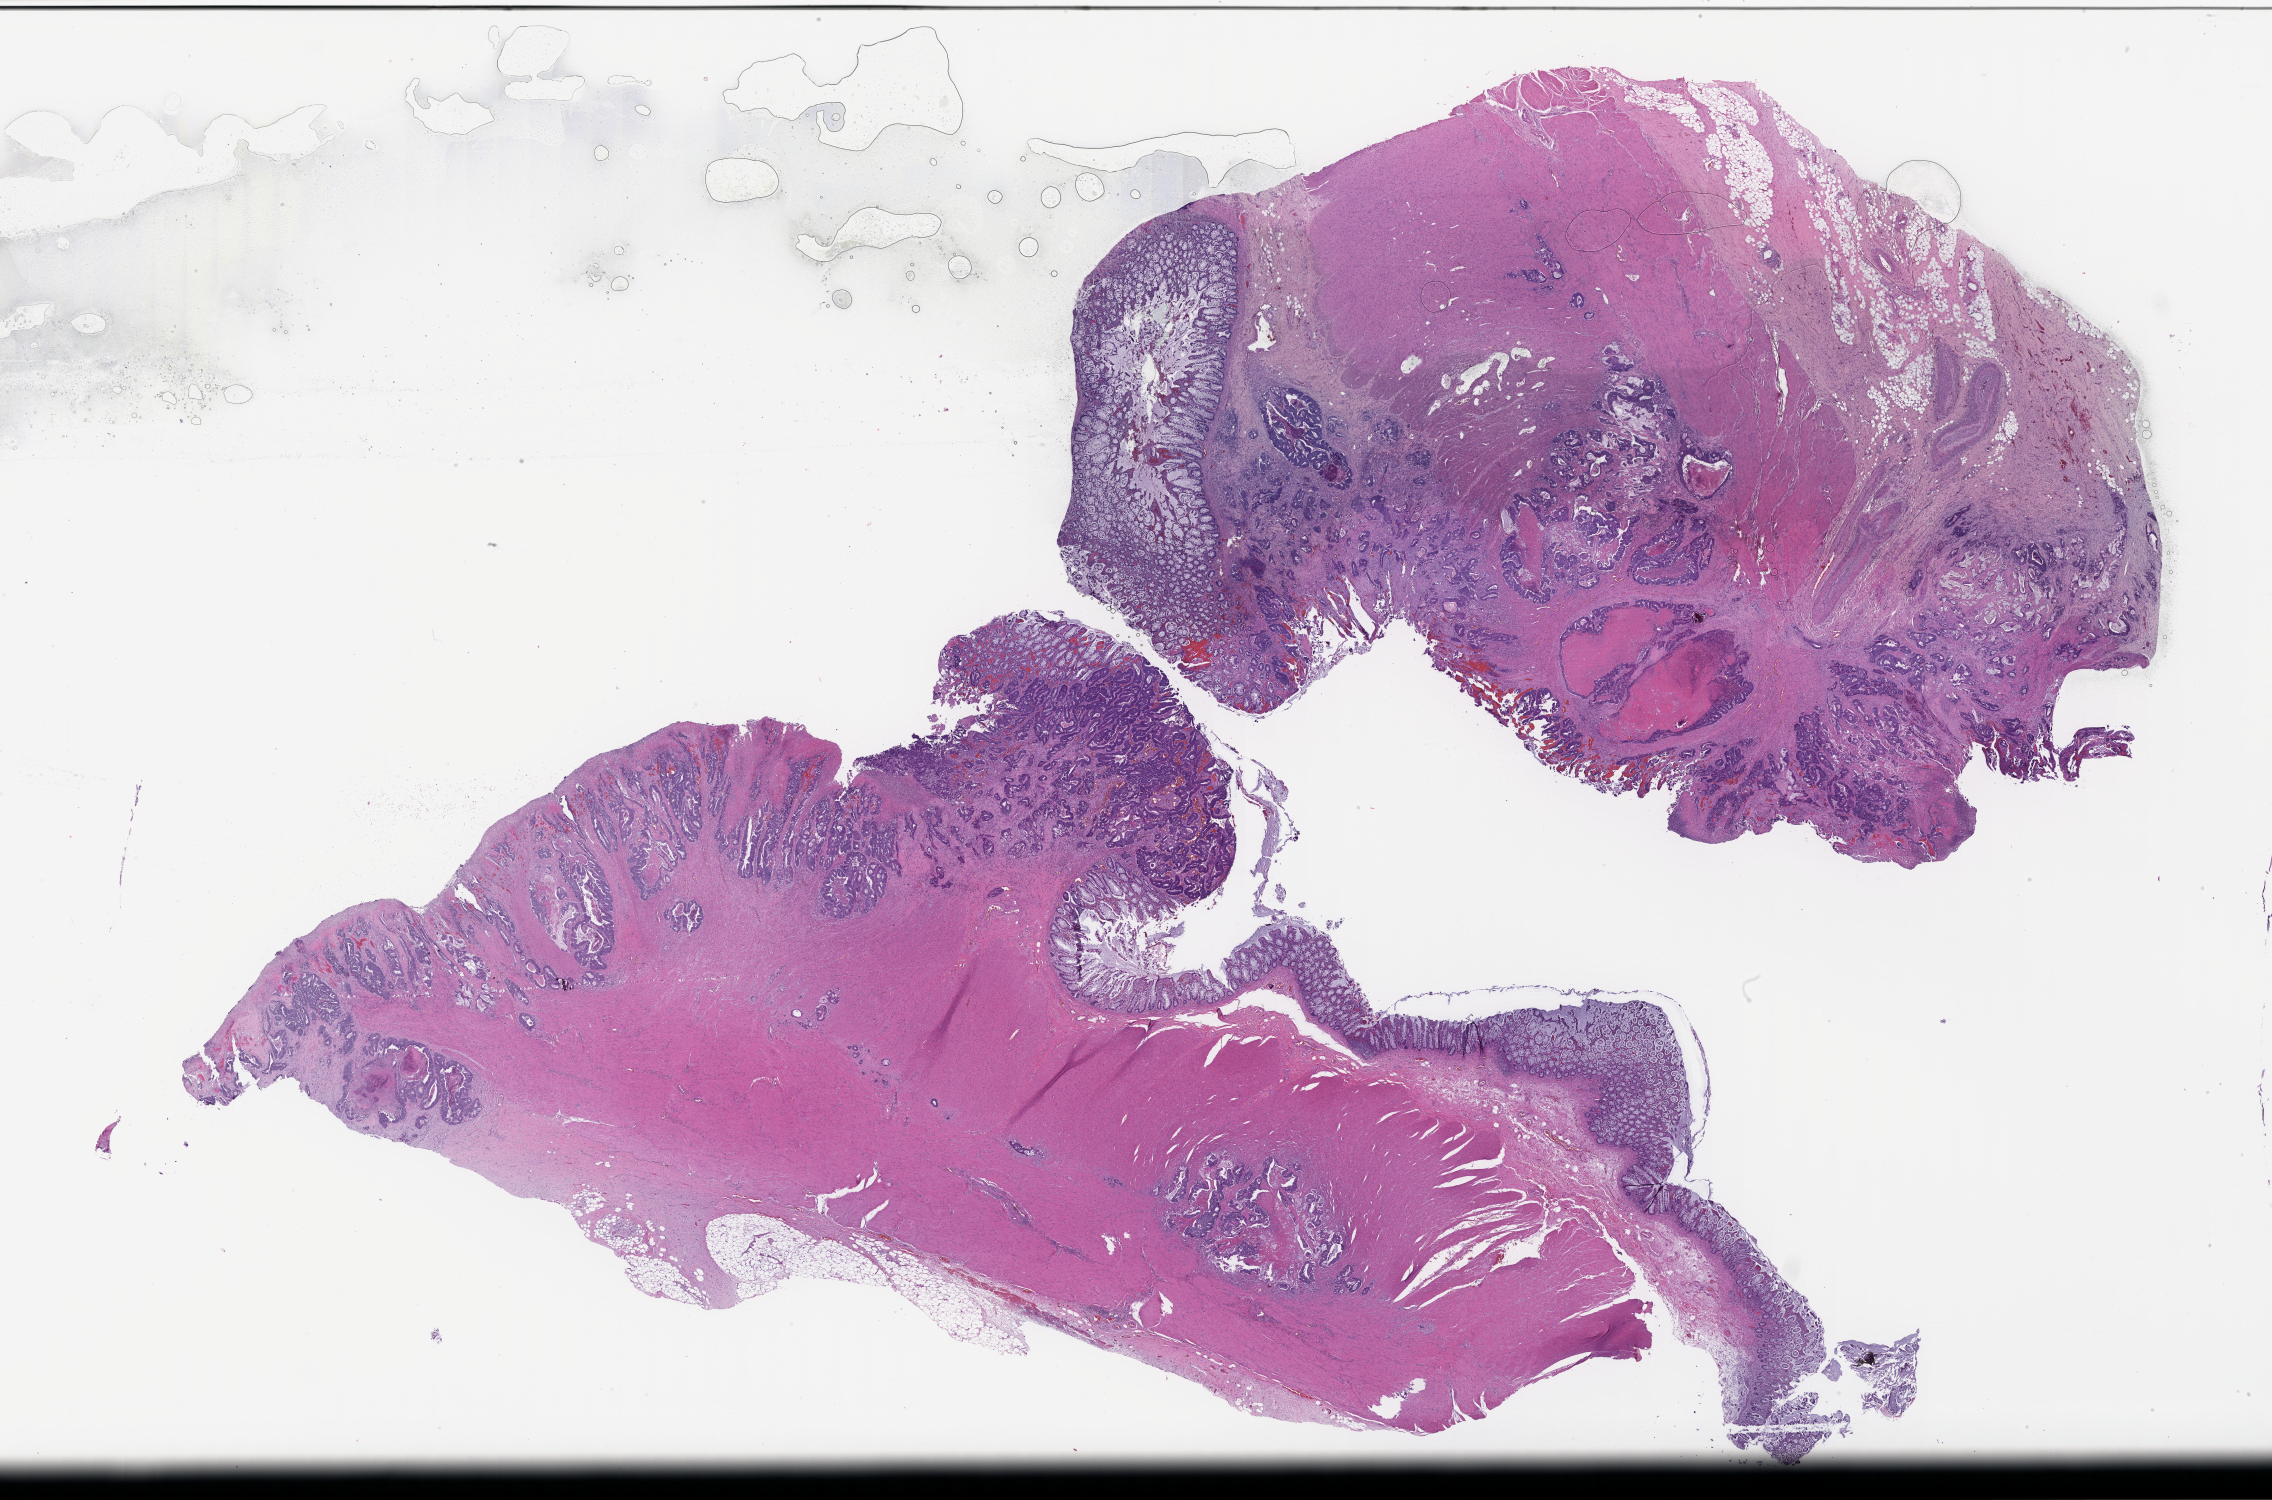
Hematoxylin and eosin (H&E) whole-slide image — whole scanned area (about 36.7 x 24.2 mm) shown as a low-resolution overview. Formalin-fixed, paraffin-embedded (FFPE) tissue. Tissue site: colon. Archival tissue. Patient sex: female.
This section: primary tumour tissue. Diagnosis: Colorectal Carcinoma.